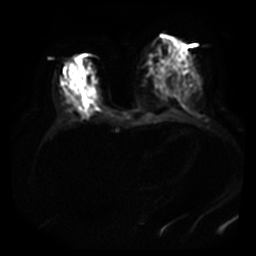
Breast MRI, one axial slice; slice 18 of 40 in the series (ordered by position); diffusion-weighted series; image 2 of 4 stored at this slice position (different b-values; order by instance number); 3 T; 256 × 256 image matrix, field of view 380 × 380 mm. Female patient.
Outlined on this slice (expert manual segmentation):
- tumour on diffusion-weighted imaging: bounding box [x1, y1, x2, y2] px = [84, 94, 90, 108]